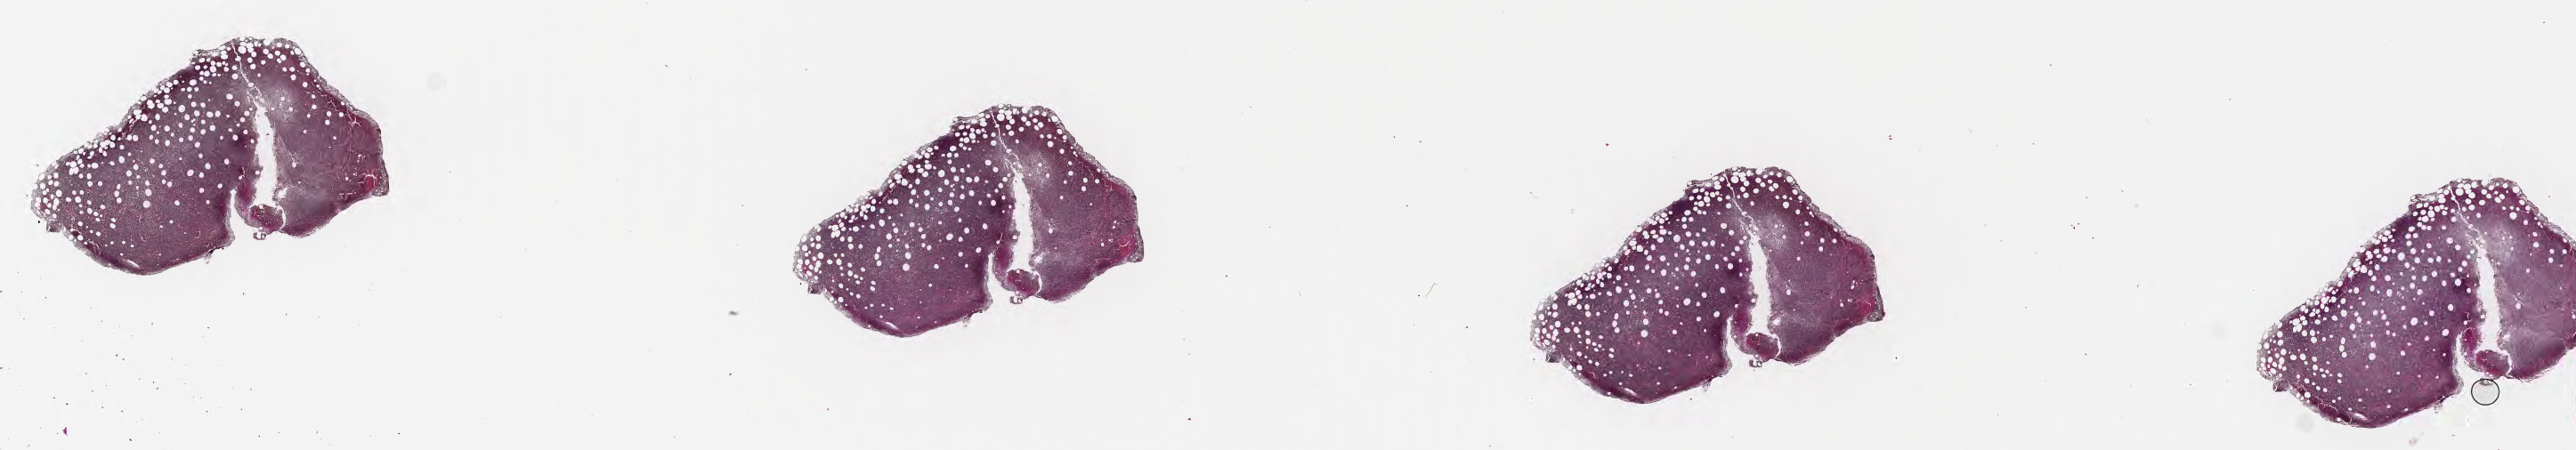
Whole-slide image, haematoxylin and eosin stain — whole scanned area (about 46.8 x 8.2 mm) shown as a low-resolution overview, formalin-fixed paraffin-embedded section, specimen: primary tumor, site: bone marrow. Male patient, 70 years old. Slide review estimates, as recorded: tumor cells 90%, tumor nuclei 90%, stromal cells 5%, necrosis 5%, normal cells 0%. Inflammatory infiltration, as recorded: lymphocyte infiltration 10%, monocyte infiltration 40%, neutrophil infiltration 20%.
- Ann Arbor stage (patient): Stage IV
- diagnosis: Neoplasm, uncertain whether benign or malignant